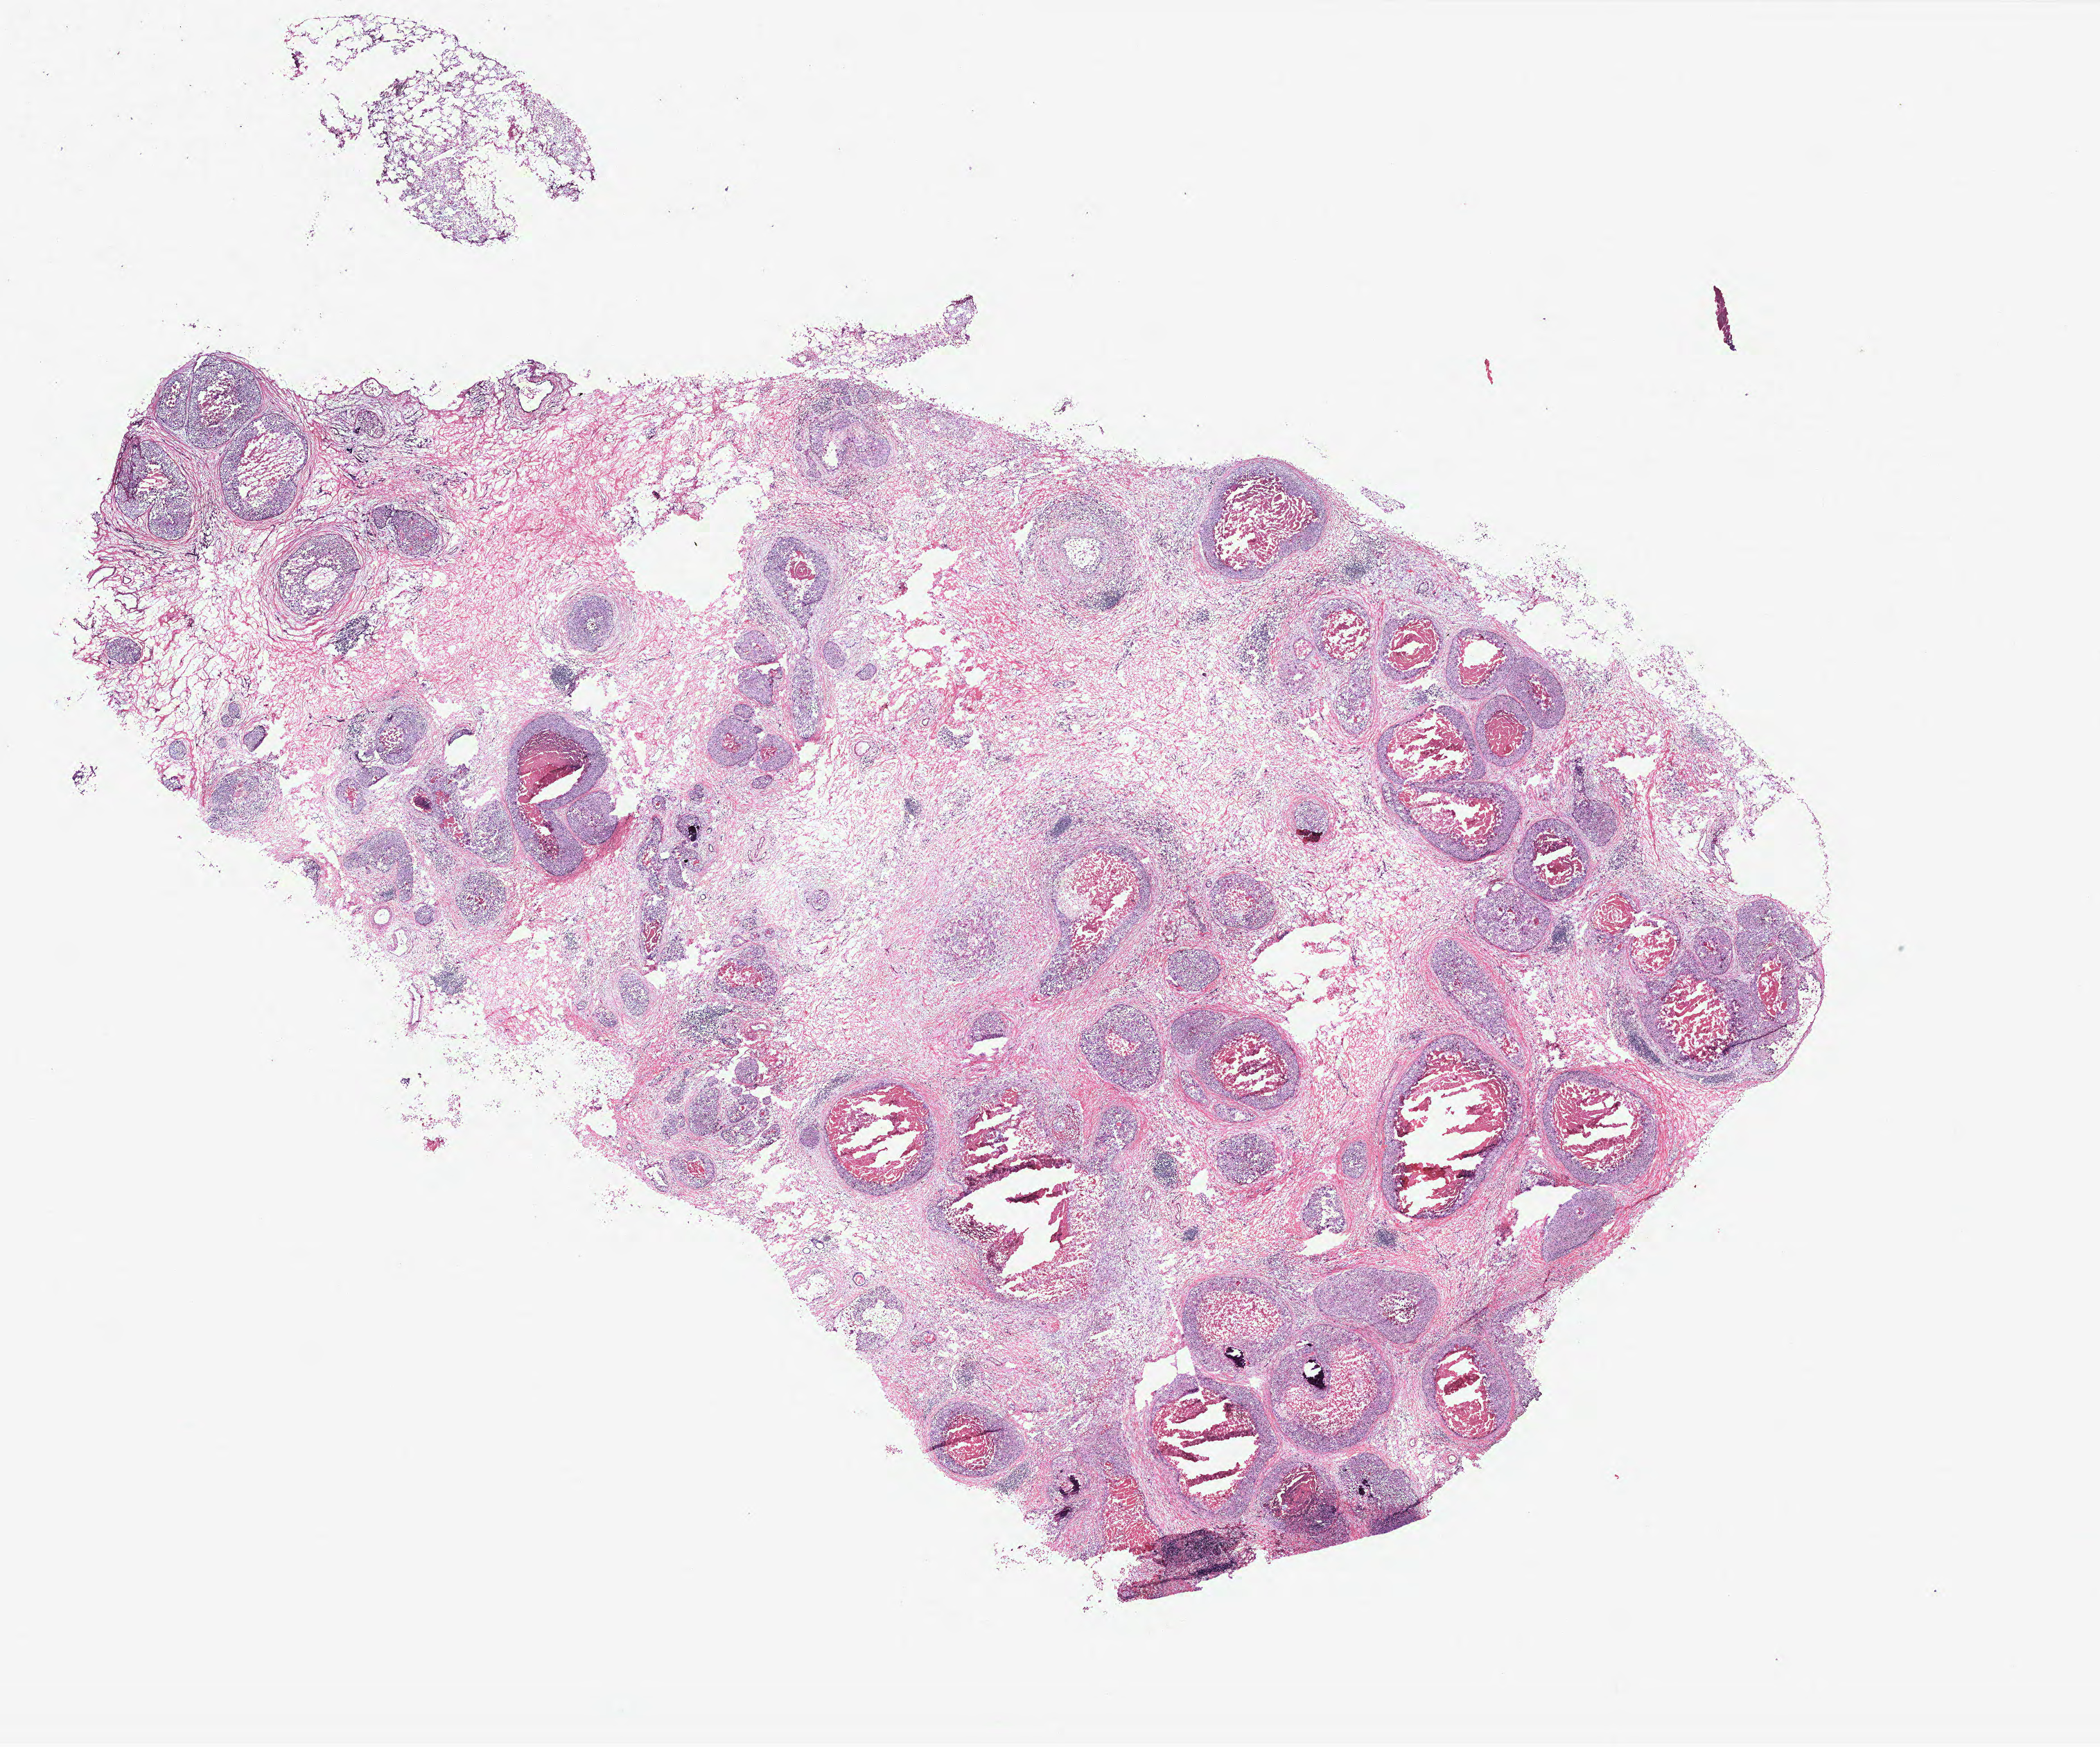
H&E-stained whole-slide image, a low-resolution overview of the entire scanned area, about 24.2 x 20.2 mm (from a 40x scan). Breast, tumour tissue. Patient: female, age 47 years.
AJCC pathologic stage: IIA. Histologic diagnosis: Infiltrating duct carcinoma, NOS.